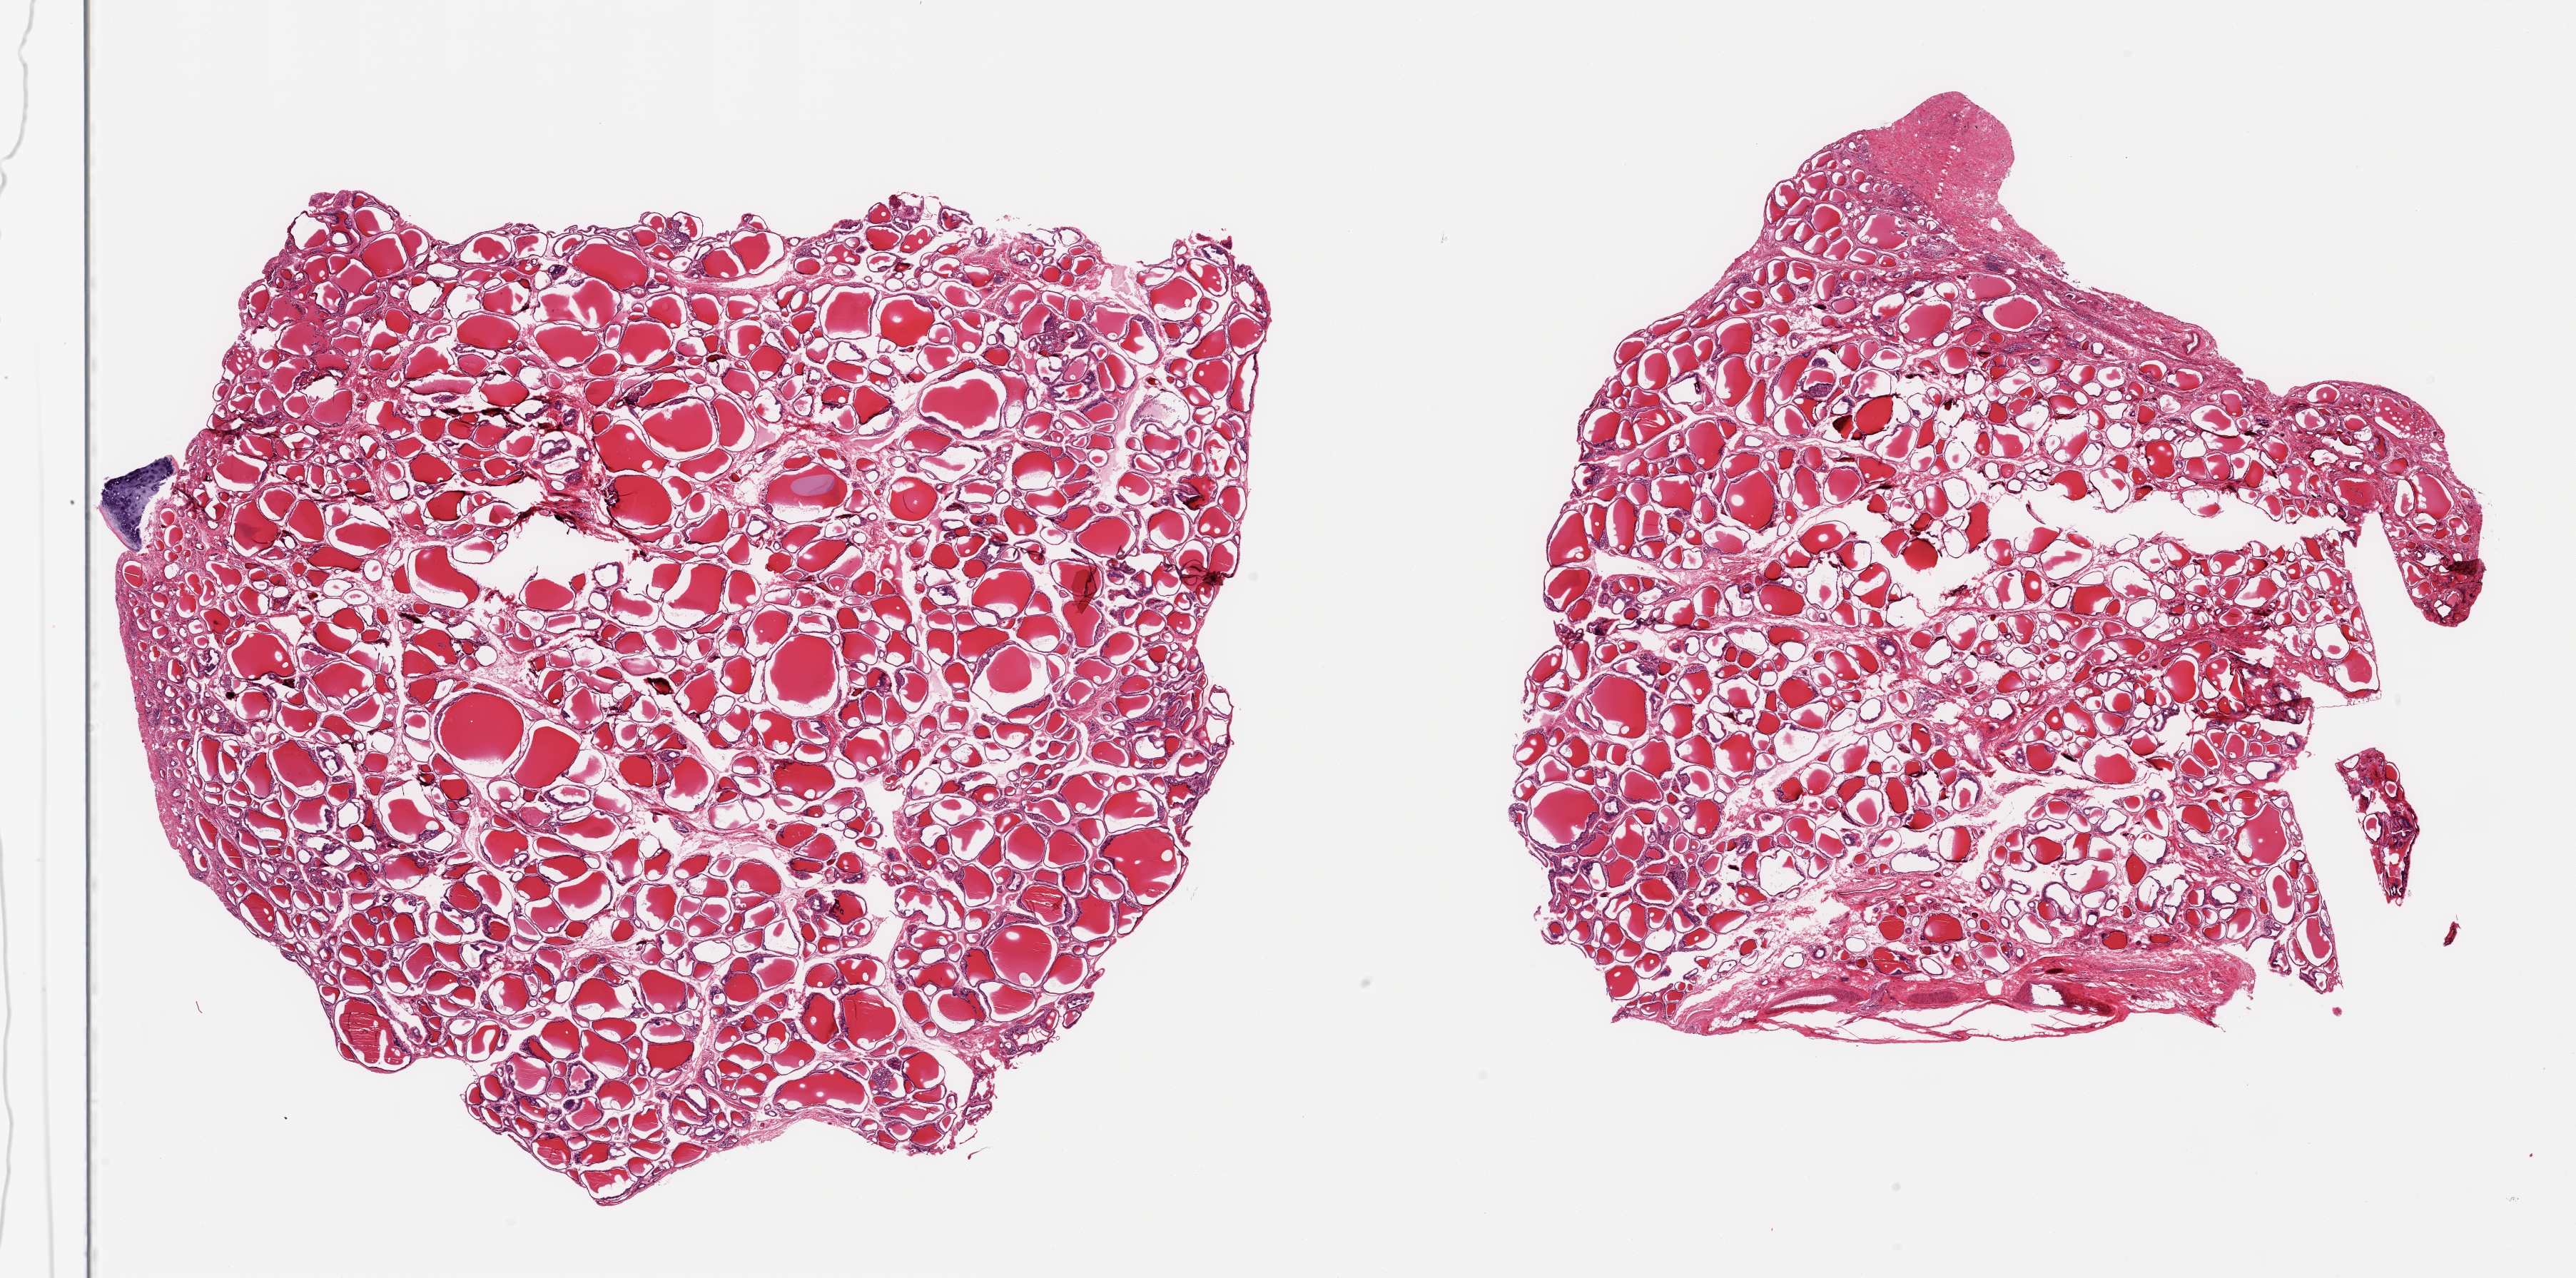
Digitized haematoxylin and eosin-stained section, brightfield, a low-resolution overview of the entire scanned area, about 28.5 x 14.2 mm (slide scanned at 20x). PAXgene-fixed paraffin-embedded (PFPE) section. Target tissue: thyroid. Tissue donor sample. Female donor.
• reviewer comment on this tissue sample: 2 pieces, no abnormality